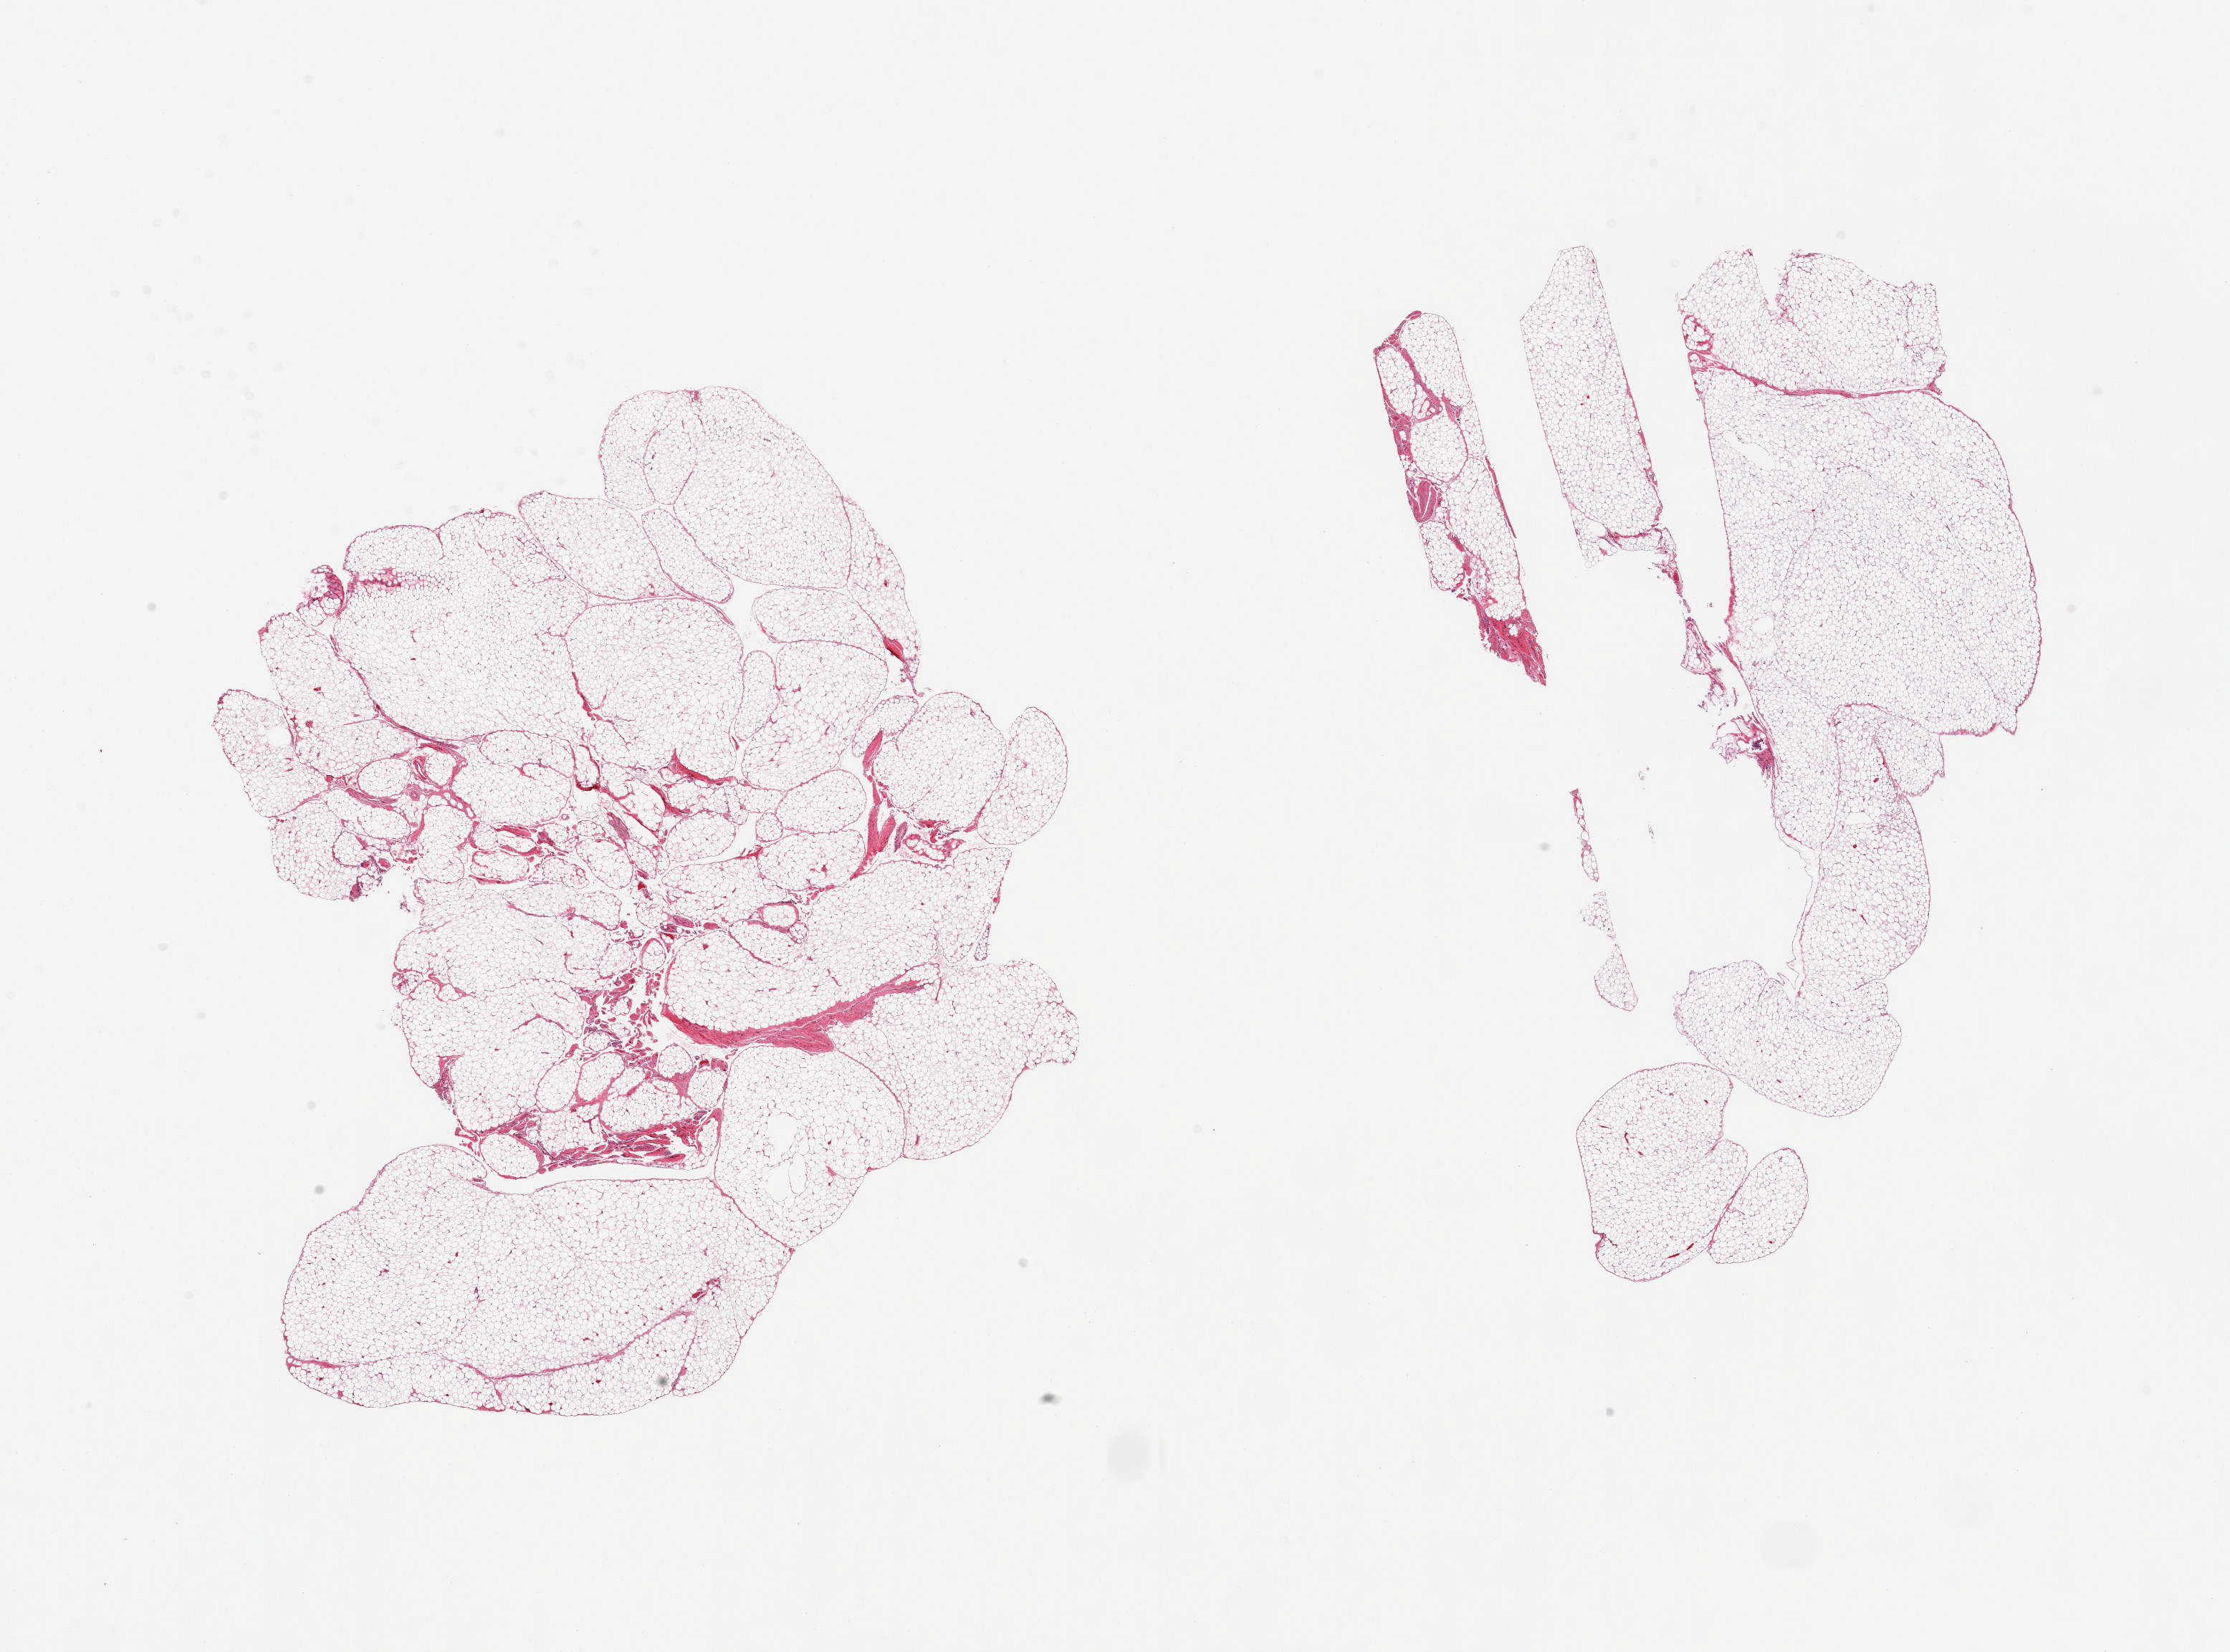
Haematoxylin and eosin whole-slide image — low-resolution overview of the scanned area, about 24.6 x 18.2 mm. PAXgene-fixed paraffin-embedded (PFPE) section. Target tissue: omentum. Donor tissue sample. Donor: male.
Reviewer comment on this tissue sample: 2 pieces; ~10% fibrovascular component.